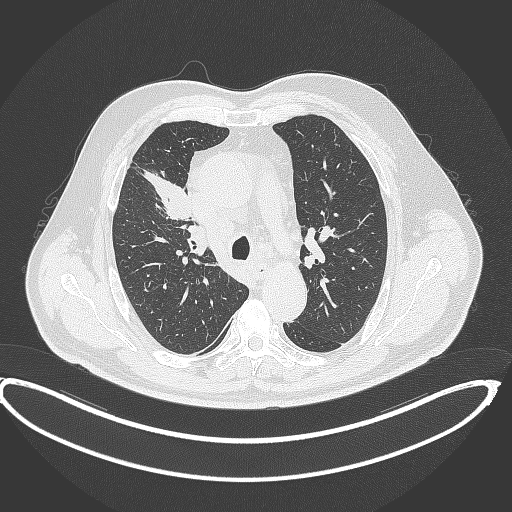
Chest CT, one axial slice; slice 281 of 390 in the series (ordered by position); reconstruction kernel B70f; 120 kVp; lung window (W 1500 / L -600 HU); 512 × 512 image matrix, field of view 448 × 448 mm. Male patient, age 62 years. Case-level facts recorded for this patient, not image findings: clinical TNM (as recorded): T1c N3 M1c.
Structures marked on this image (rectangle marked by the reading radiologist):
- lung tumour (recorded histology: adenocarcinoma): bounding box [x1, y1, x2, y2] px = [141, 166, 192, 220]